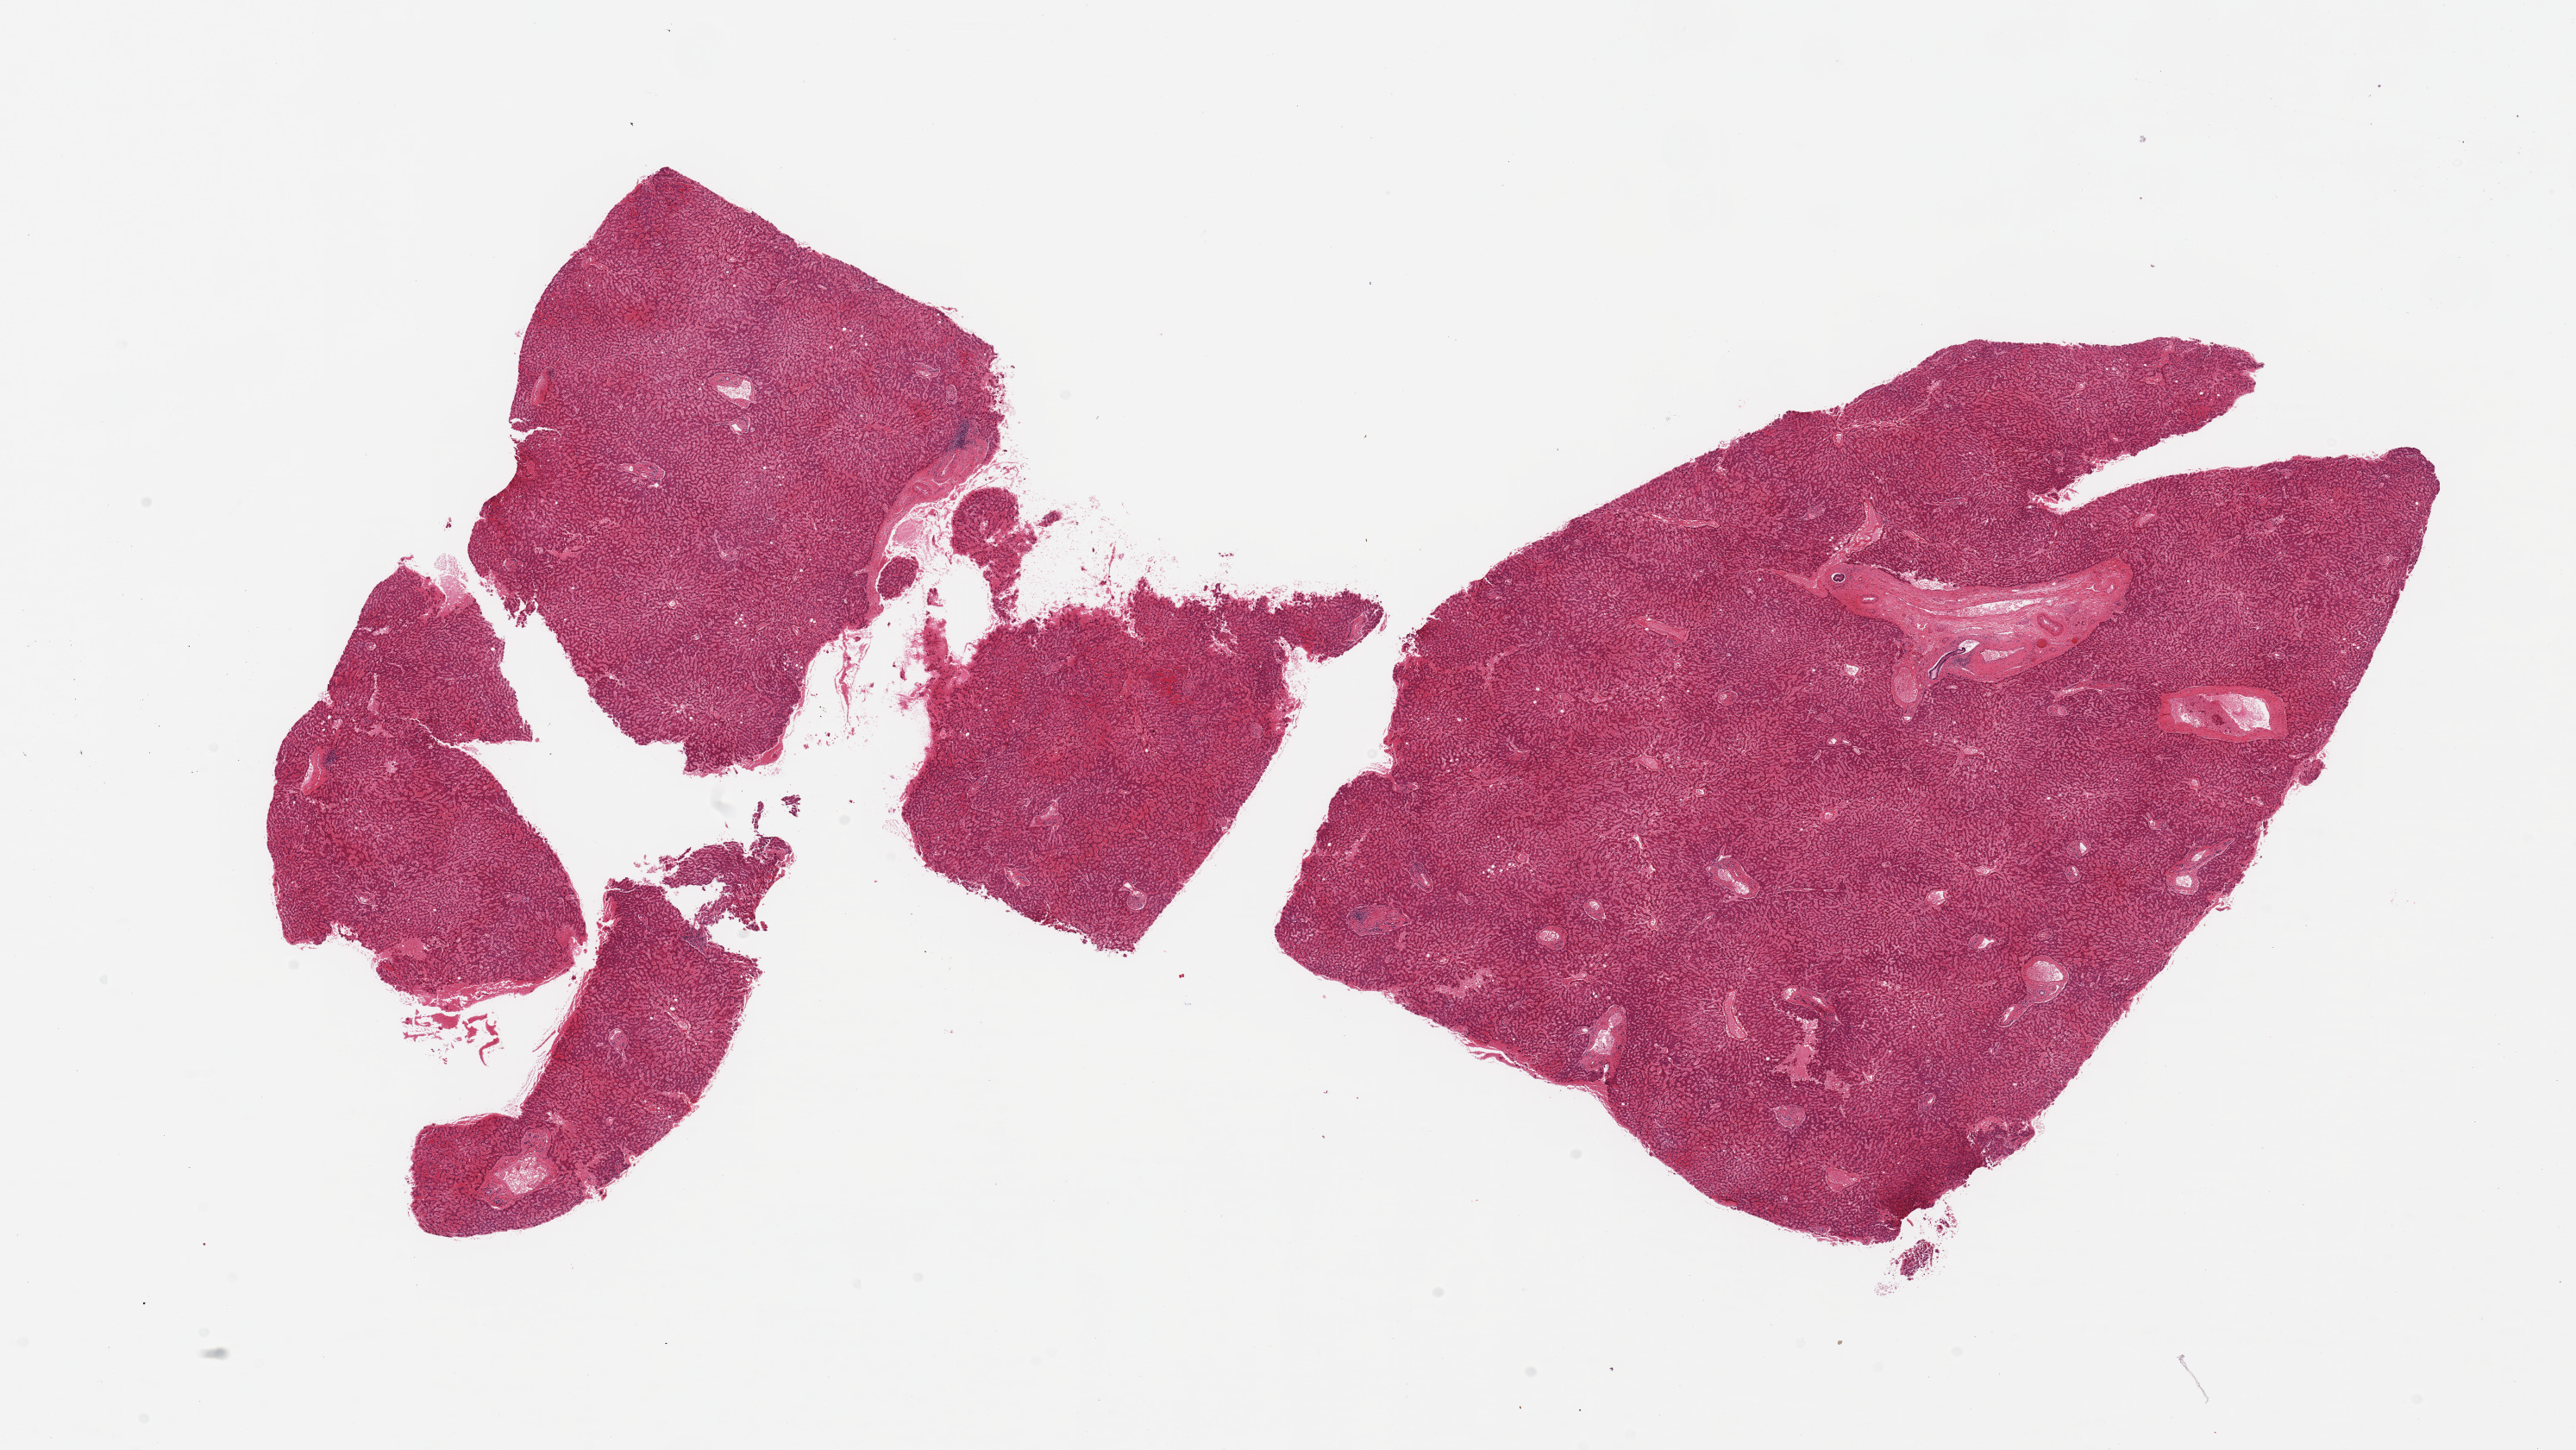
Whole-slide image, H&E stain, brightfield — low-resolution overview of the scanned area, about 23.6 x 13.3 mm (acquisition: 20x scan), PAXgene-fixed, paraffin-embedded tissue, section of liver (target tissue), donor tissue sample. Male donor.
• review note (as recorded): 2 pieces, mild congestion